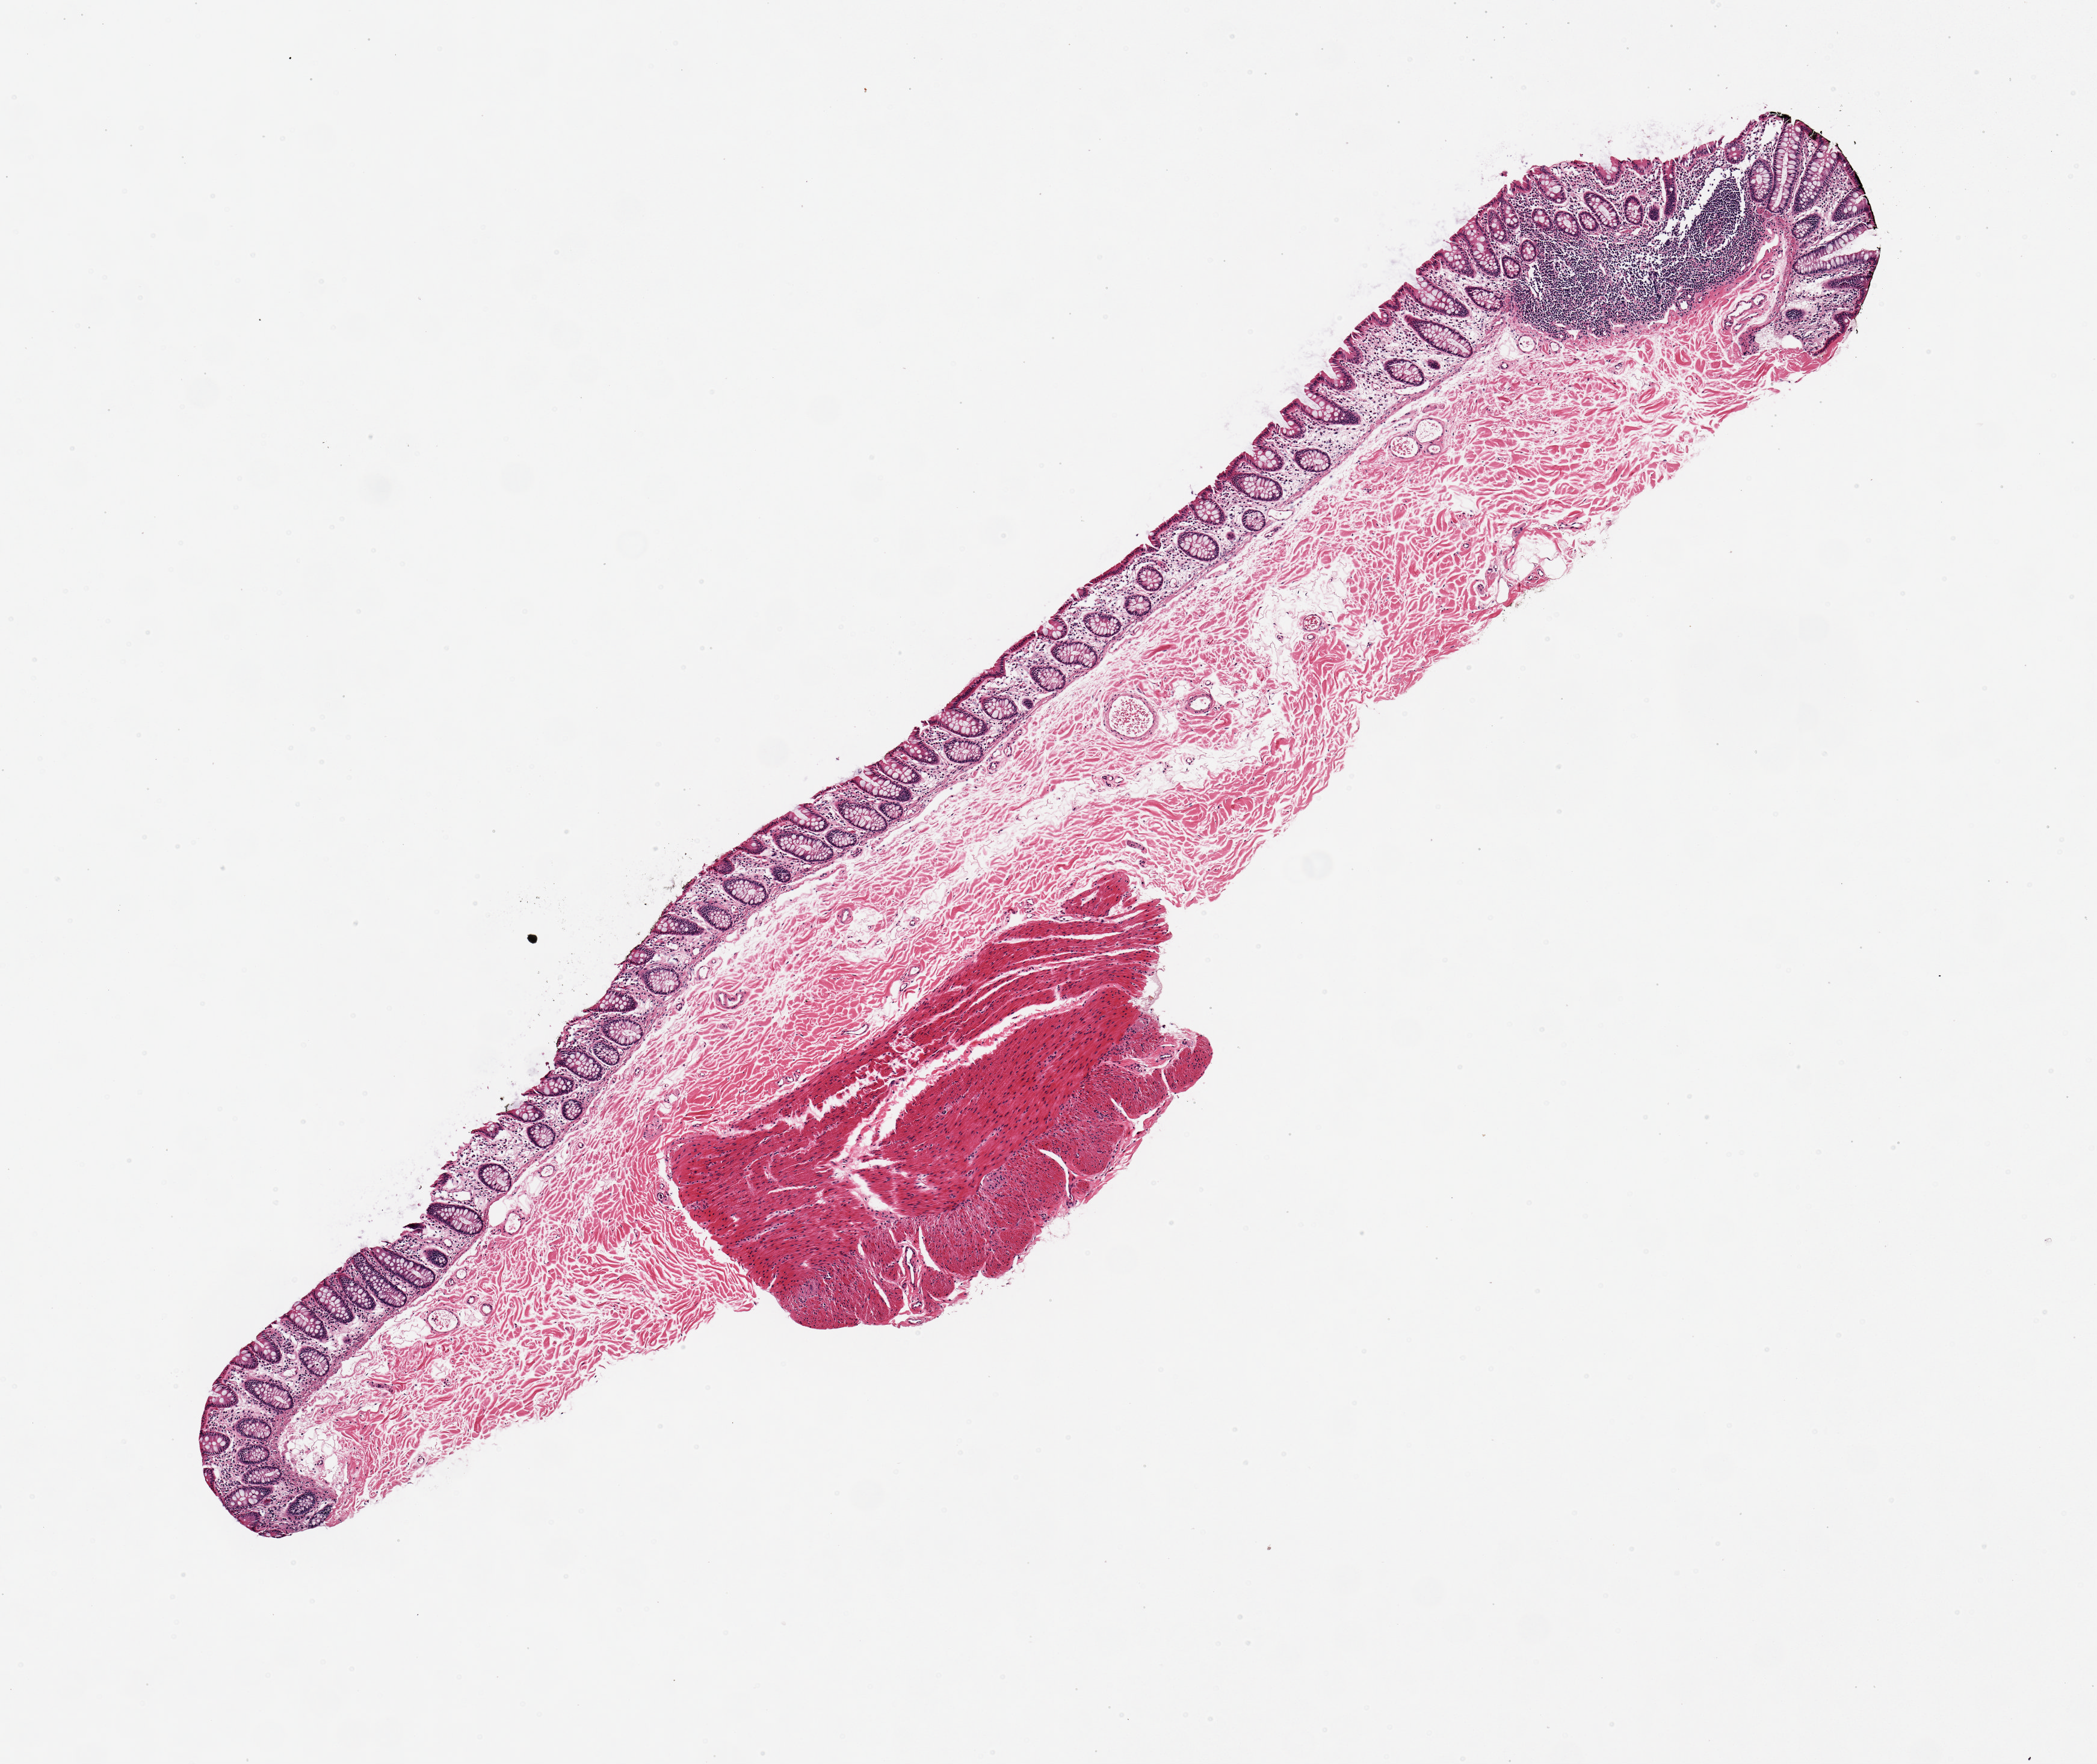
Digitized haematoxylin and eosin-stained section, whole scanned area (about 6.9 x 5.8 mm) shown as a low-resolution overview, PAXgene-fixed, paraffin-embedded tissue, section of transverse colon (target tissue), tissue donor sample. Donor sex: male.
Review note (as recorded): 1 piece with small amount (1.6x0.8 mm) muscularis propria.